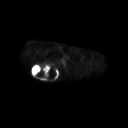
FDG PET of an extremity soft-tissue mass (from a PET/CT study), one axial slice. Slice 197 of 267 in the series (ordered by position). 3.27 mm slice thickness. 128 × 128 image matrix, field of view 700 × 700 mm. Male patient, age 61 years. Case-level facts recorded for this patient, not image findings: histological type: pleiomorphic spindle cell undifferentiated; grade: high; site of the primary tumour: right parascapusular.
Outlined on this slice (expert contour drawn on MRI and transferred to this co-registered scan by the dataset authors):
- gross tumour volume including surrounding oedema: box from (x=31, y=64) to (x=60, y=79) px
- gross tumour volume (mass): (x=31, y=64)–(x=58, y=78)